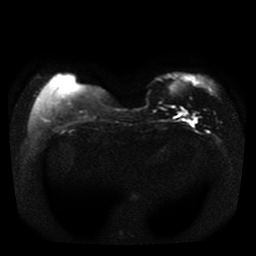
Breast MRI, one axial slice; slice 9 of 41 in the series (ordered by position); diffusion-weighted series; image 2 of 4 stored at this slice position (different b-values; order by instance number); 1.5 T; 5 mm slice thickness; 256 × 256 image matrix, field of view 330 × 330 mm. Female patient.
Outlined on this slice (expert manual segmentation):
- tumour on diffusion-weighted imaging: bounding box [x1, y1, x2, y2] px = [179, 111, 188, 117]